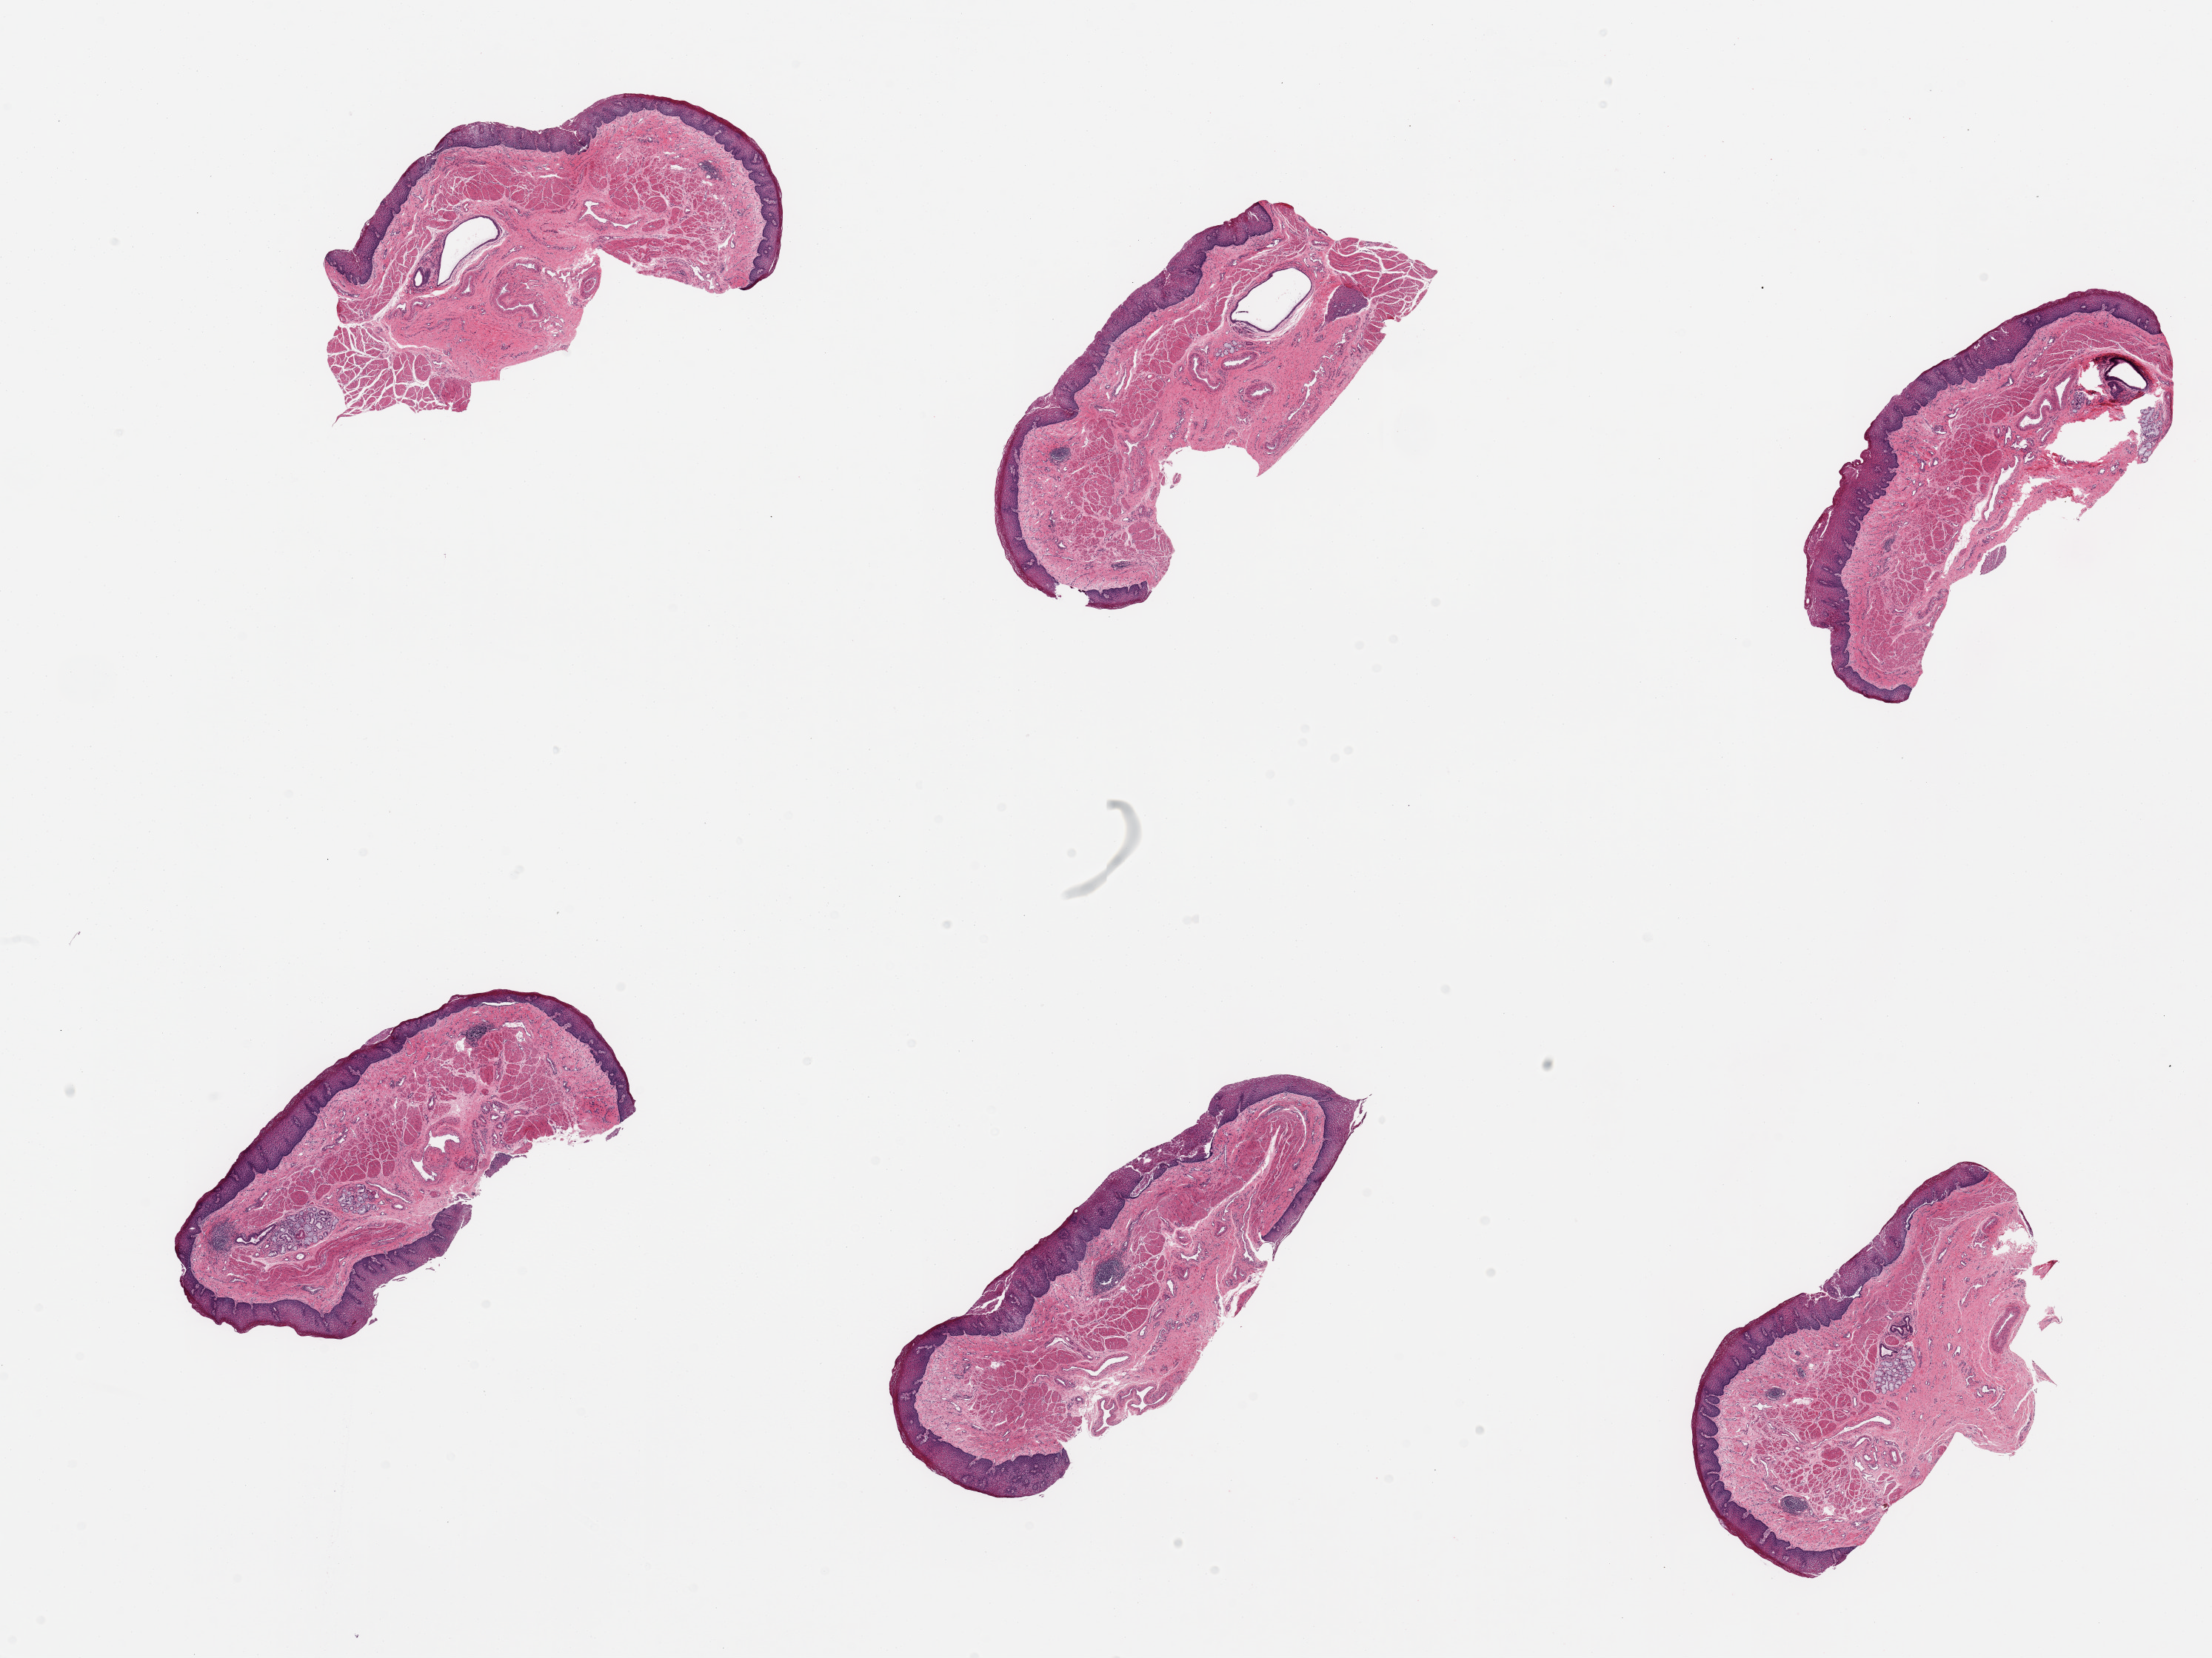
H&E whole-slide image — whole scanned area (about 23.6 x 17.7 mm, acquisition: 20x scan) shown as a low-resolution overview. PAXgene-fixed, paraffin-embedded tissue. Sampled site (target tissue): esophageal mucous membrane. Donor tissue sample. Donor: male.
Pathologist's review note for this sample: 6 pieces; mild focal chronic esophagitis.